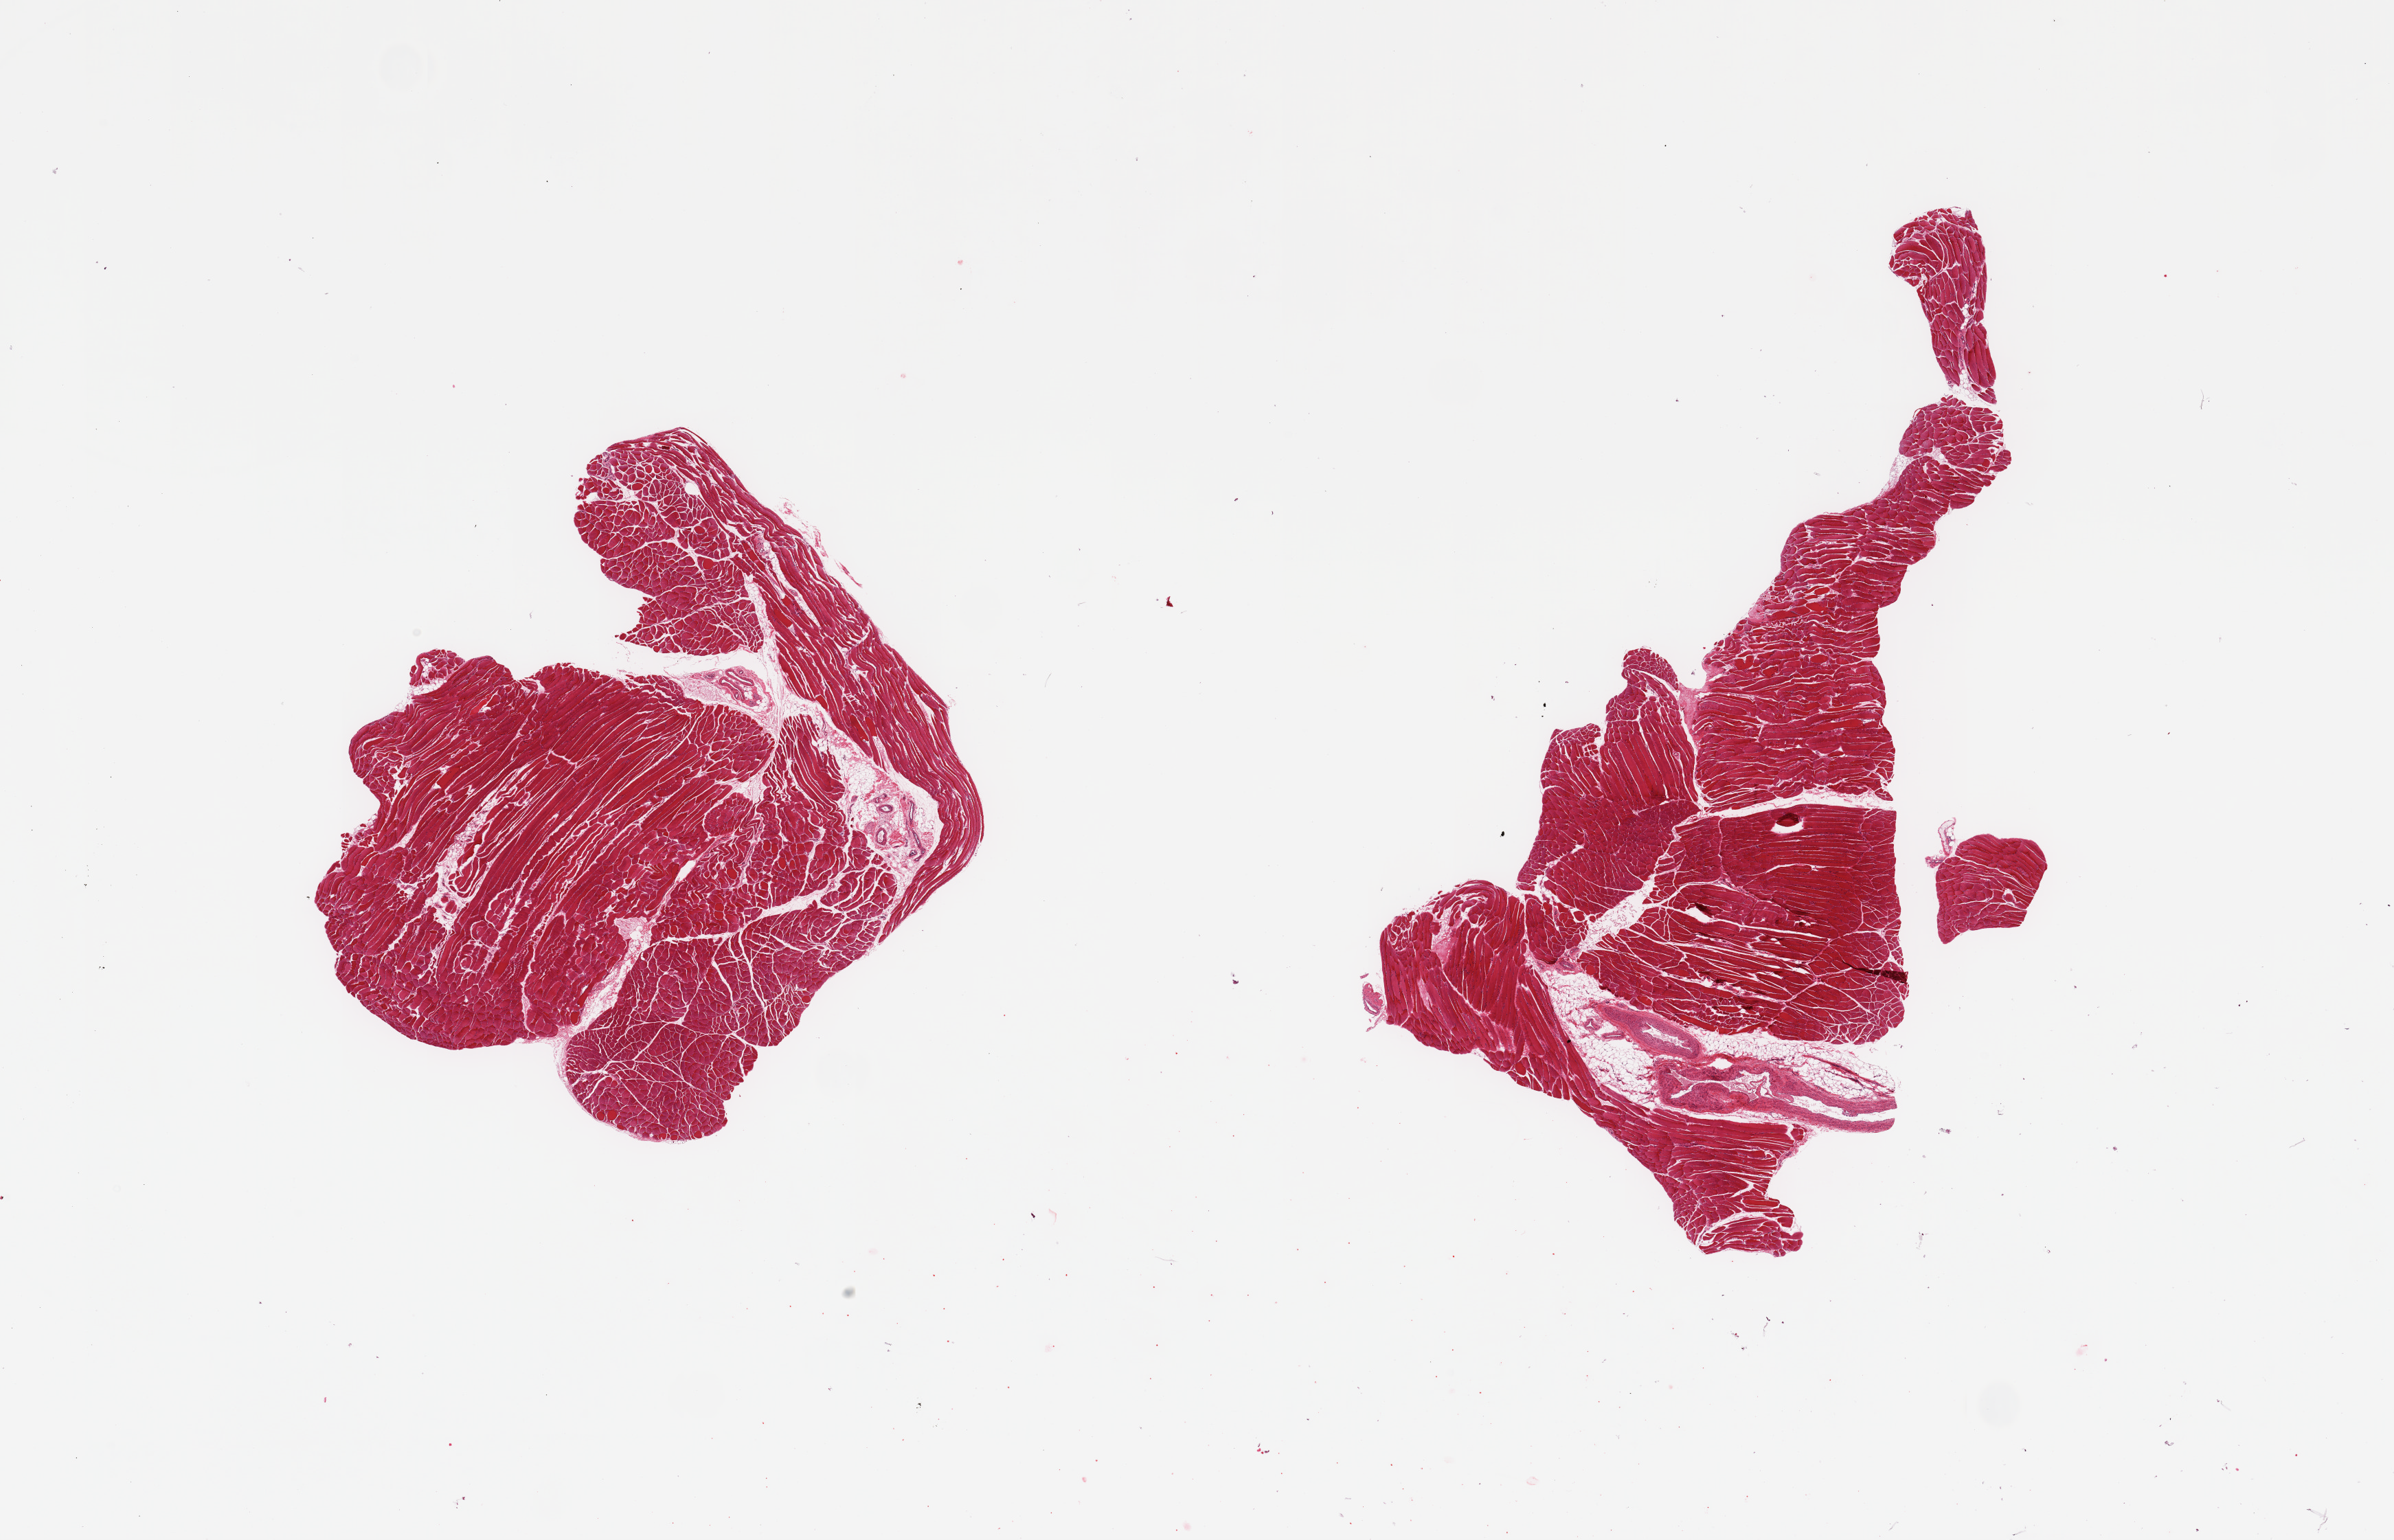
Whole-slide image, hematoxylin and eosin (H&E) stain, brightfield, low-resolution overview of the scanned area, about 27.6 x 17.7 mm (from a 20x scan); PAXgene-fixed paraffin-embedded (PFPE) section; section of skeletal muscle (target tissue); donor tissue sample.
Pathologist's review note for this sample: 2 pieces; internal large vessels & fat comprise 15% & 5%.